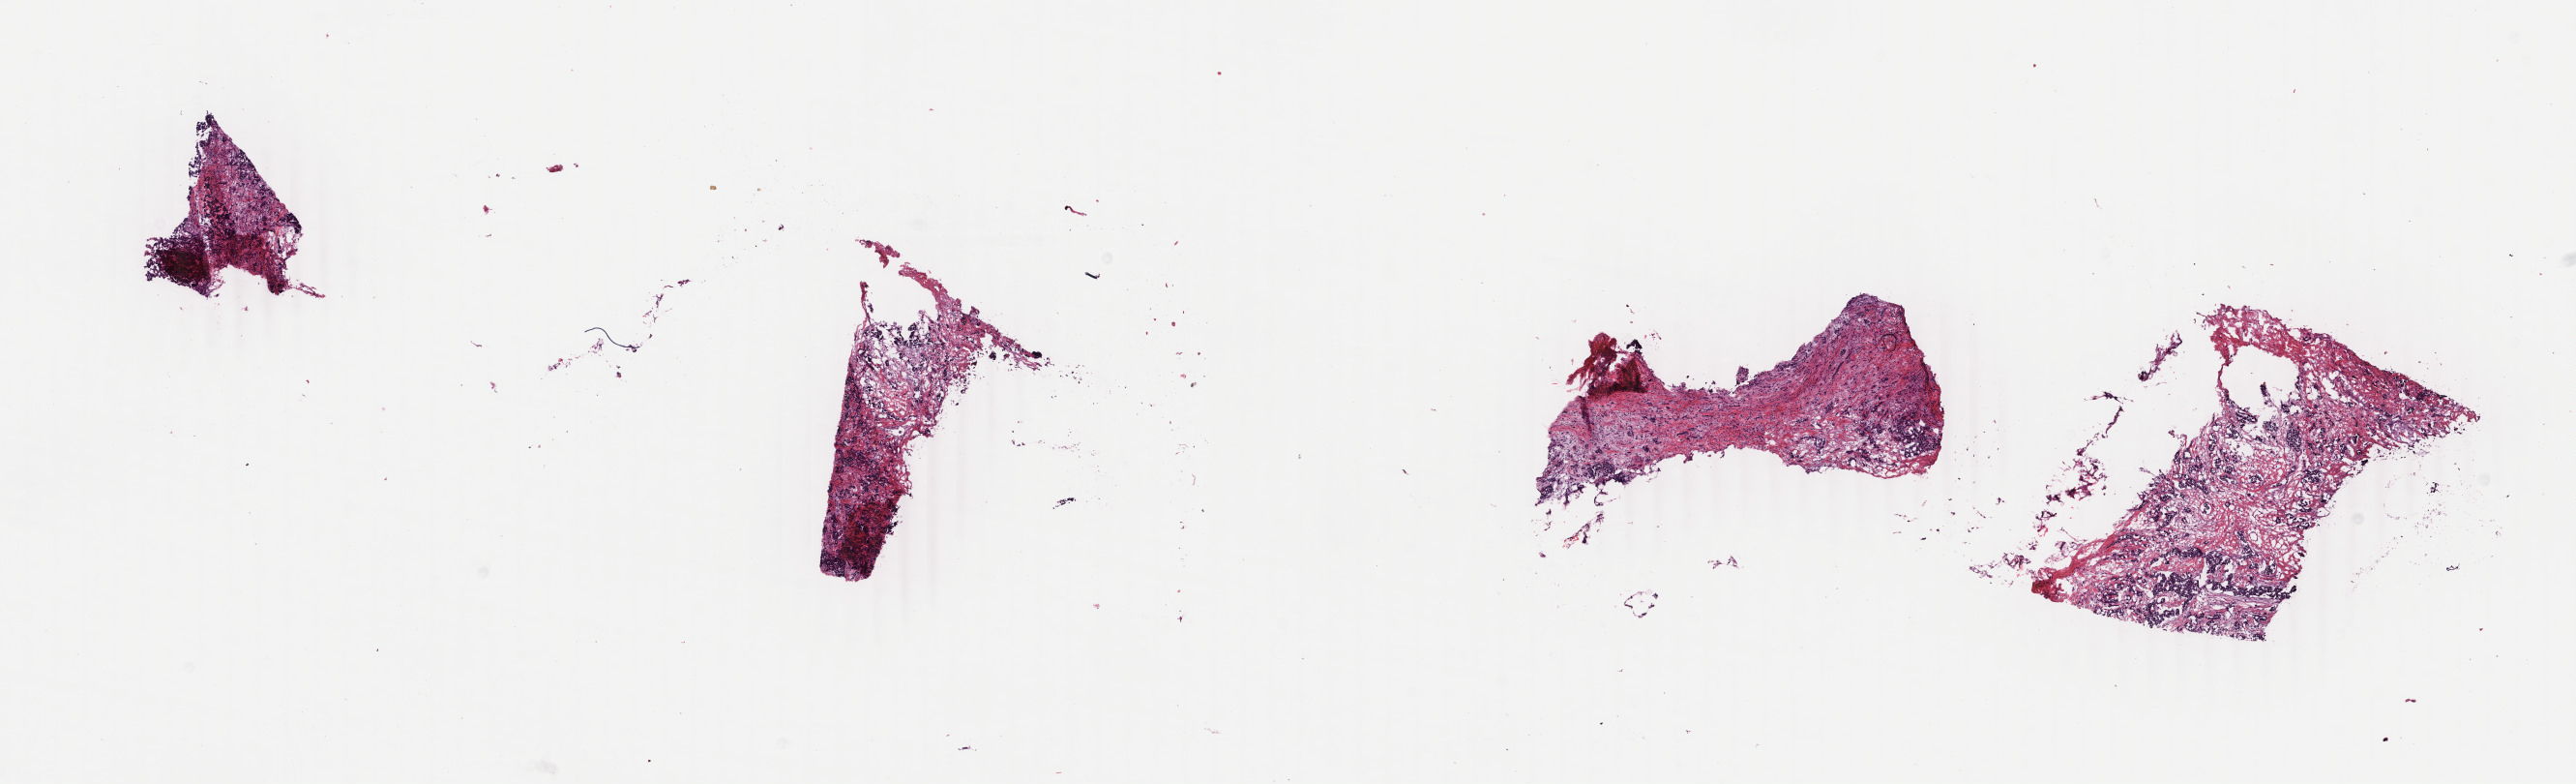
Digitized H&E tissue section (whole slide) — whole scanned area (about 21.2 x 6.4 mm) shown as a low-resolution overview, frozen section from the bottom of the tissue portion, sample: primary tumour, breast. Patient: female, age at initial diagnosis 60 years. Slide review estimates, as recorded: tumour cells 75%, tumour nuclei 75%, normal cells 0%, stromal cells 24%, necrosis 1%. Infiltration values recorded for this section: lymphocyte infiltration 2%, monocyte infiltration 0%, neutrophil infiltration 0%.
- AJCC pathologic stage: IIA
- lymph nodes positive (case pathology): 0 of 16 examined
- pathologic diagnosis: Infiltrating duct carcinoma, NOS
- laterality: left
- TNM: T2 N0 (i-) M0